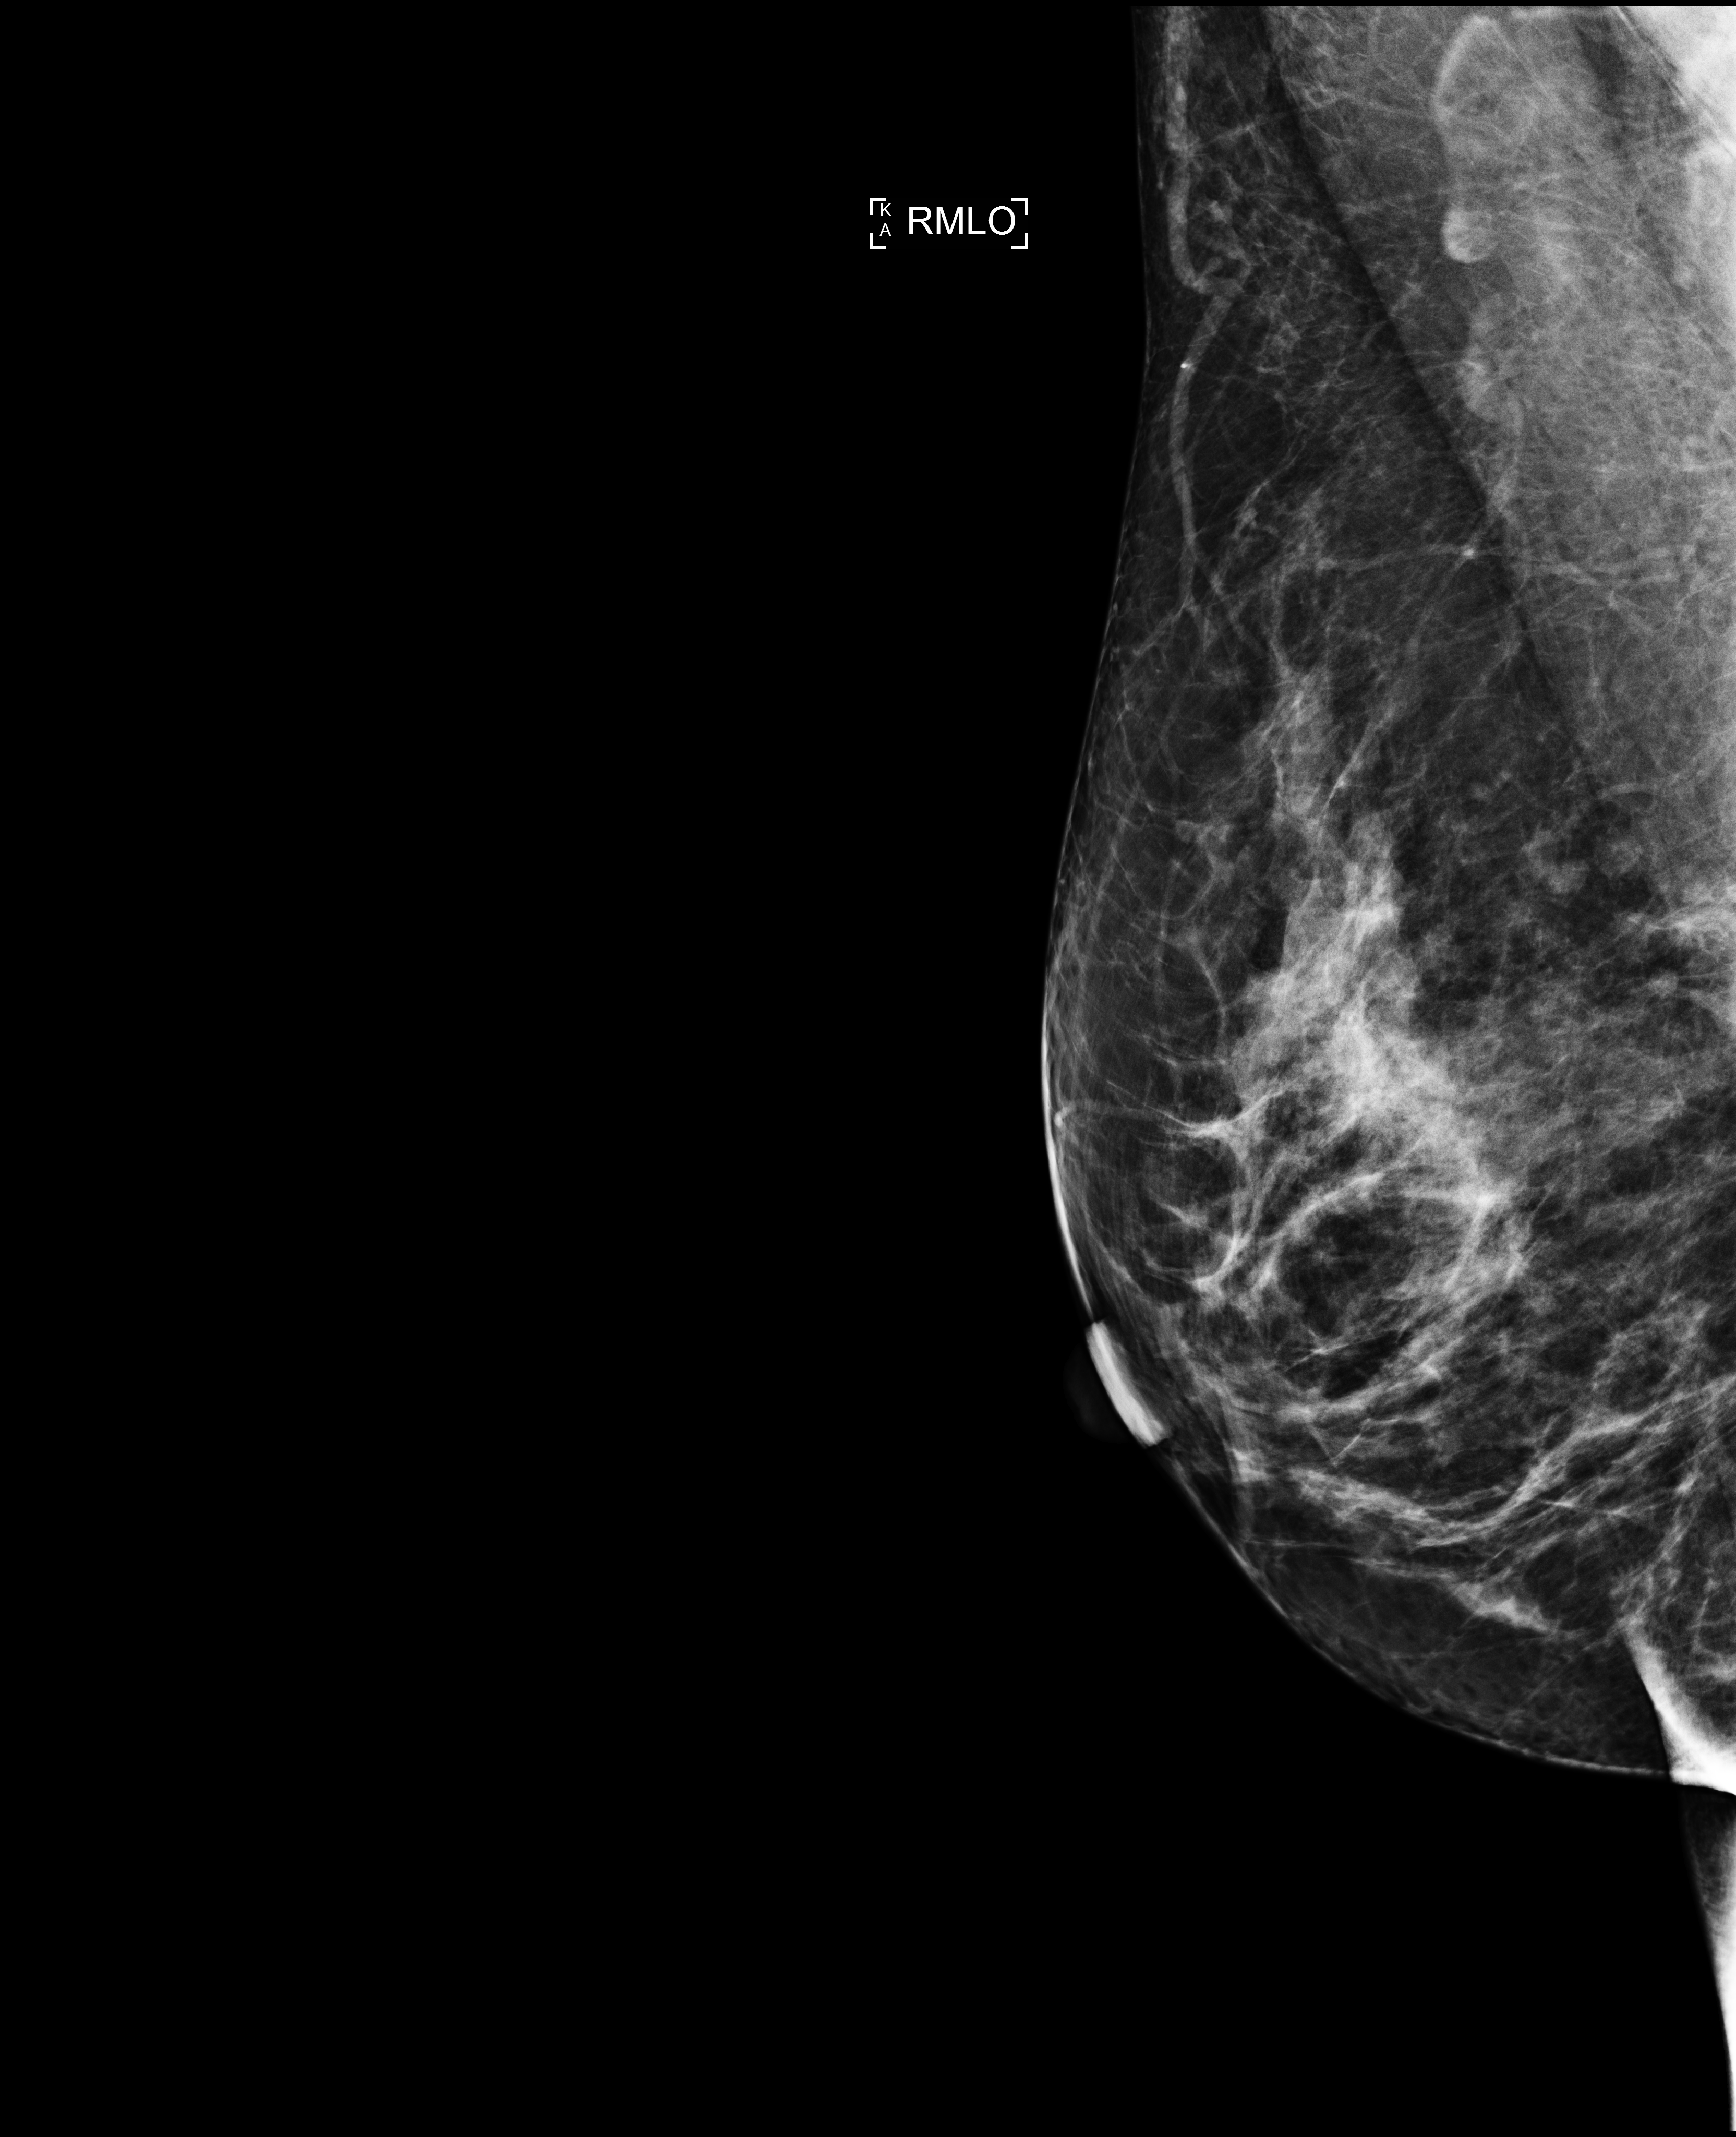
Annual screening mammography examination. Patient aged 47 years (female).
Image type: full-field digital mammogram. Breast: right. Projection: medio-lateral oblique projection.